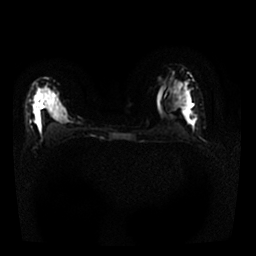
Breast MRI, one axial slice; position 16 of 25 along the scan axis; diffusion-weighted series; image 2 of 4 stored at this slice position (different b-values; order by instance number); 1.5 T; 4 mm slice thickness; 256 × 256 image matrix. Female patient.
Outlined on this slice (outlined manually by an expert reader):
- tumour on diffusion-weighted imaging: bounding box [x1, y1, x2, y2] px = [36, 96, 40, 105]